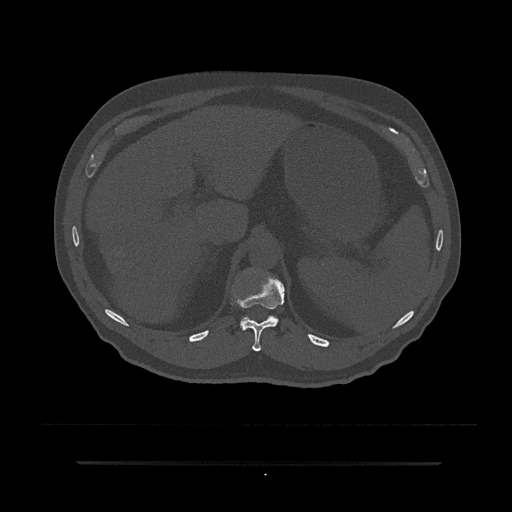
CT including the spine, one axial slice; position 250 of 797 along the scan axis; reconstruction kernel Br40s/3; bone window (W 1800 / L 400 HU); 0.5 mm slice thickness; 512 × 512 image matrix, field of view 464 × 464 mm. Patient: male, 59 years. From the clinical record (not read from this slice): primary cancer: bile ducts; vertebrae with lytic lesions (as recorded): T10.
Structures marked on this image (semi-automatically segmented with operator editing):
- T11 vertebra: bounding box (x1, y1, x2, y2) in pixels: (232, 275, 284, 352)
- T12 vertebra: (240, 316, 278, 328)